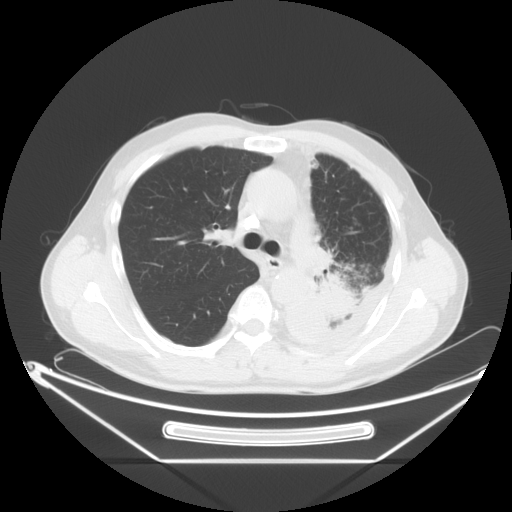
Chest CT, one axial slice; reconstruction kernel STANDARD; 120 kVp; lung window (W 1500 / L -600 HU); 5 mm slice thickness; 512 × 512 image matrix. Patient: male, 60 years. From the clinical record (not read from this slice): clinical TNM (as recorded): T4 N1 M1.
Annotated regions visible in this slice (bounding box drawn by a radiologist):
- lung tumour (recorded histology: adenocarcinoma): bounding box <307,256,370,334> (left, top, right, bottom; pixels)